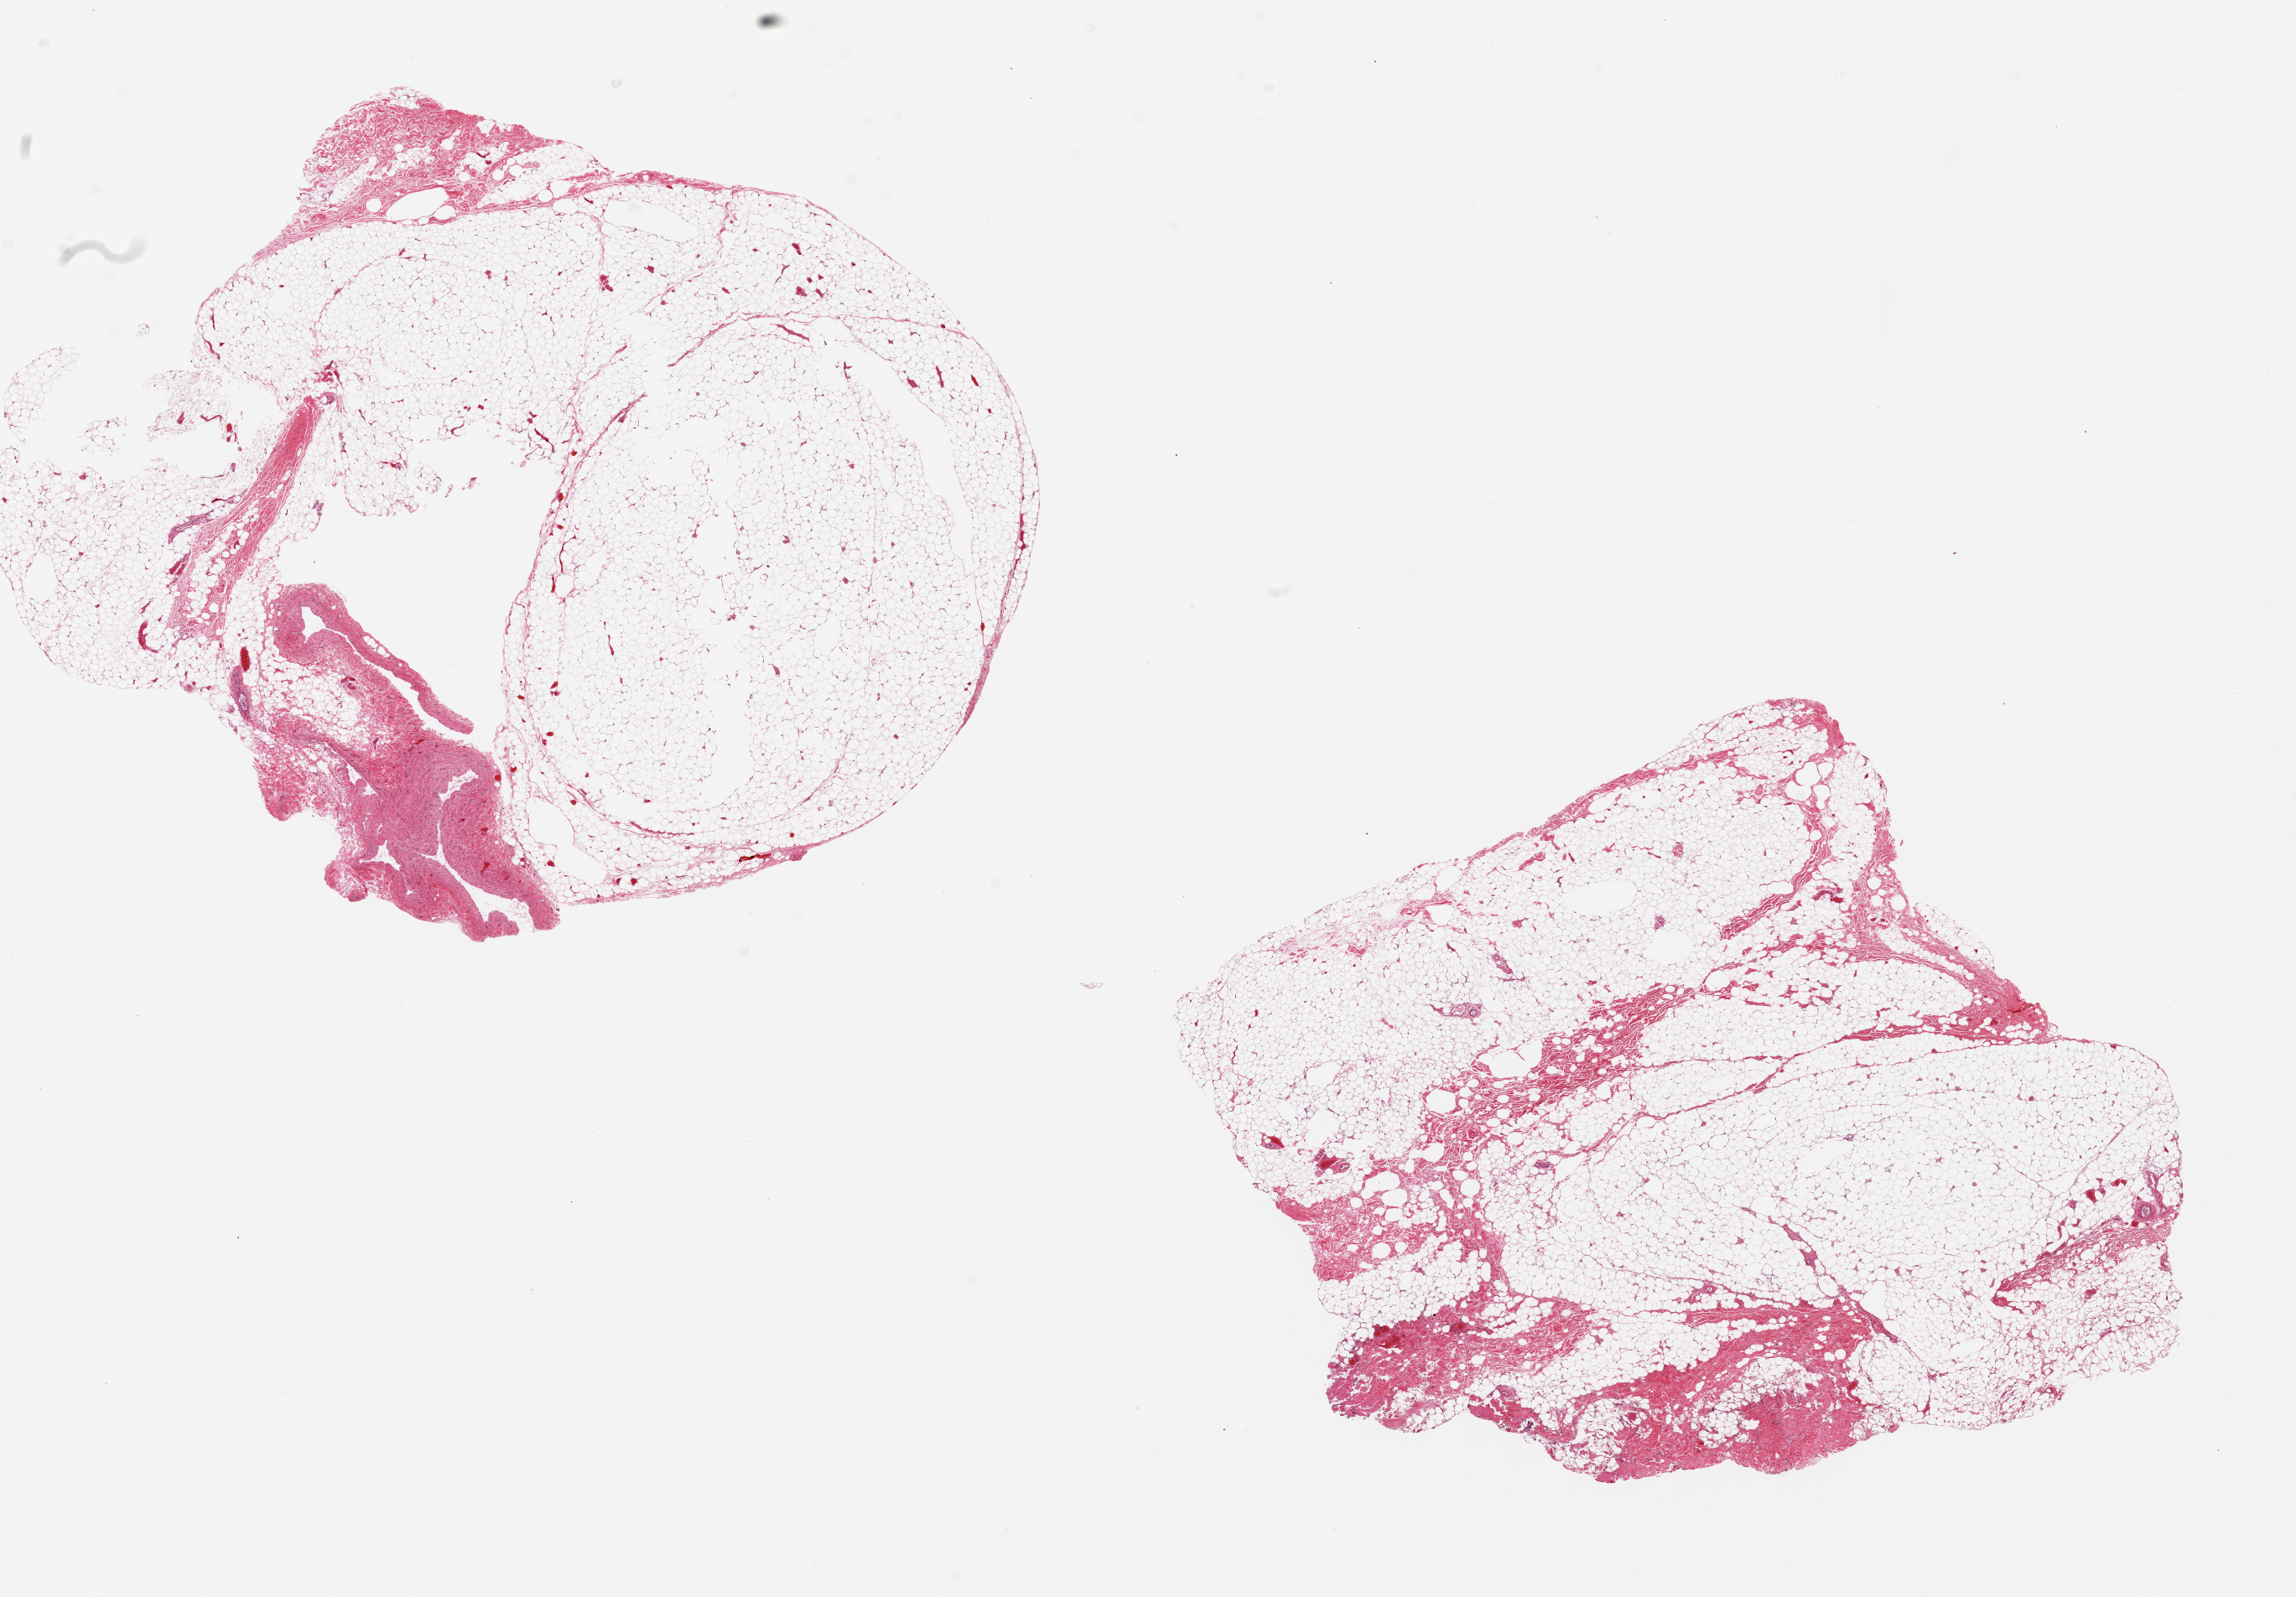
H&E whole-slide image — whole scanned area (about 21.7 x 15.1 mm) shown as a low-resolution overview, PAXgene-fixed, paraffin-embedded tissue, target tissue: thyroid, tissue donor sample. Male donor.
Reviewer comment on this tissue sample: 2 pieces, no thyroid tissue, fibroadipose tissue of unknown provenance.